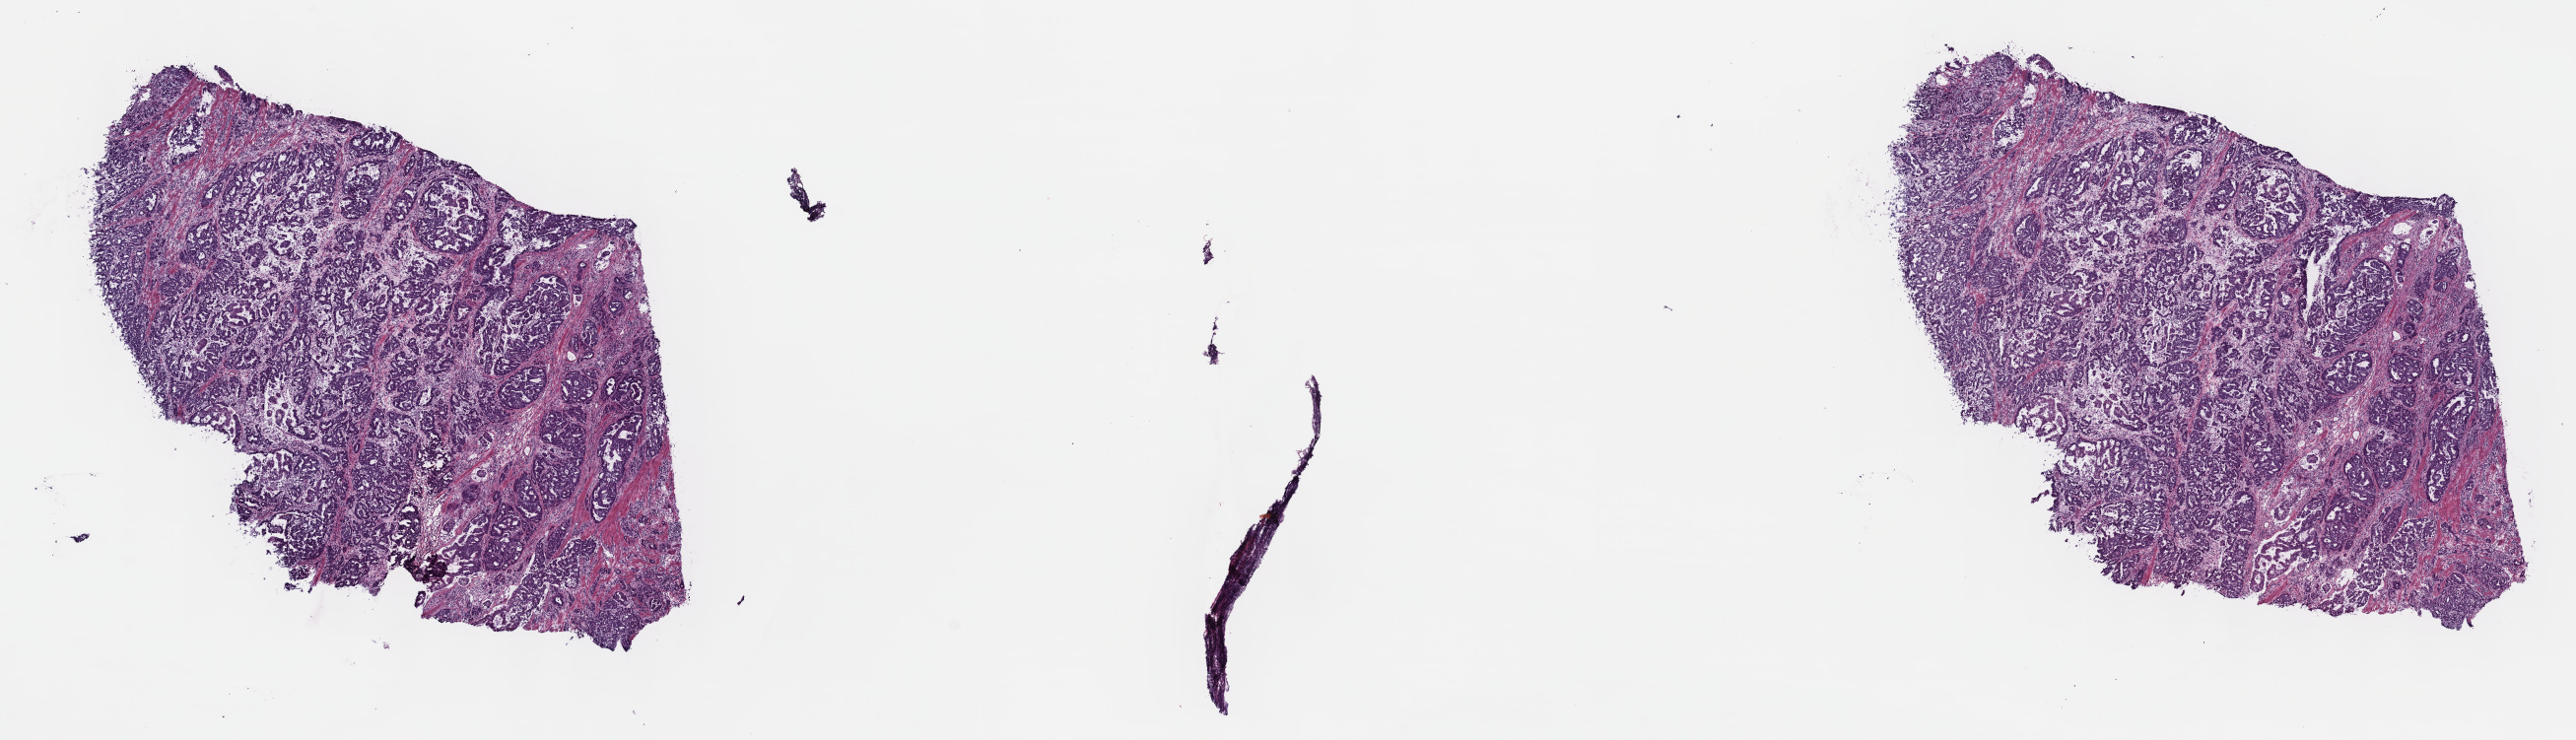
Whole-slide histology image, Hematoxylin and eosin (H&E) stained — a low-resolution overview of the entire scanned area, about 21.1 x 6.1 mm. Frozen section from the top of the tissue portion. Sample: primary tumour, stomach. Patient: male, age at initial diagnosis 68 years. Histologic grade: G3 (poorly differentiated). Pathologist review of this section (percent, as recorded): tumour cells 100%, tumour nuclei 65%, normal cells 0%, stromal cells 0%, necrosis 0%. Inflammatory infiltration, as recorded: lymphocyte infiltration 3%, monocyte infiltration 0%, neutrophil infiltration 0%.
TNM: T3 N3 M0. AJCC pathologic stage: IIIB. Diagnosis: Adenocarcinoma, NOS (cardia, NOS). Lymph nodes positive (case pathology): 9 of 16 examined.